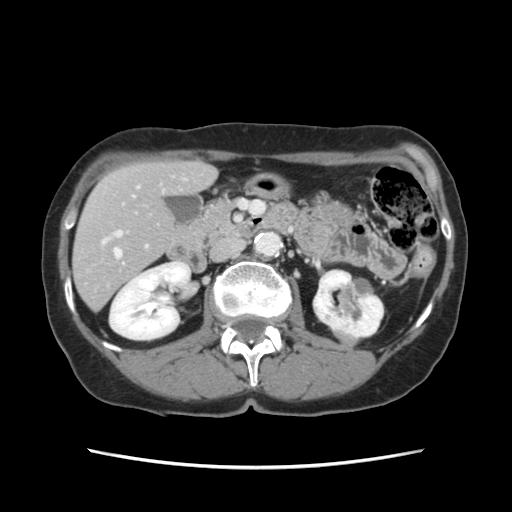
Contrast-enhanced abdominal CT, one axial slice; position 51 of 120 along the scan axis; 120 kVp; intravenous contrast given; soft-tissue window (W 400 / L 40 HU); 512 × 512 image matrix, field of view 330 × 330 mm. Female patient, age 70 years. From the clinical record (not read from this slice): diagnosis: colorectal cancer liver metastases, imaged before liver resection; multiple liver metastases: no; largest metastasis: 2.5 cm; chemotherapy before resection: yes.
Annotated regions visible in this slice (outlined manually by an expert reader):
- hepatic veins: bounding box <114,249,121,258> (left, top, right, bottom; pixels)
- liver: <74,162,215,309>
- planned liver remnant (the part of the liver to remain after resection): <74,162,215,308>
- portal vein (with intrahepatic branches): <101,179,185,248>